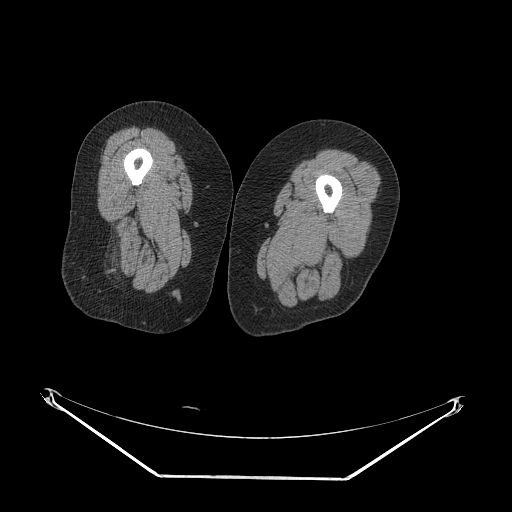
CT of an extremity soft-tissue mass (from a PET/CT study), one axial slice. Slice 21 of 257 in the series (ordered by position). Reconstruction kernel STANDARD. 140 kVp. Soft-tissue window (W 400 / L 40 HU). 512 × 512 image matrix, field of view 500 × 500 mm. Female patient. Case-level facts recorded for this patient, not image findings: histological type: synovial sarcoma; grade: intermediate; site of the primary tumour: right buttock.
Annotated regions visible in this slice (expert contour drawn on MRI and transferred to this co-registered scan by the dataset authors):
- gross tumour volume including surrounding oedema: bounding box [x1, y1, x2, y2] px = [94, 240, 113, 275]